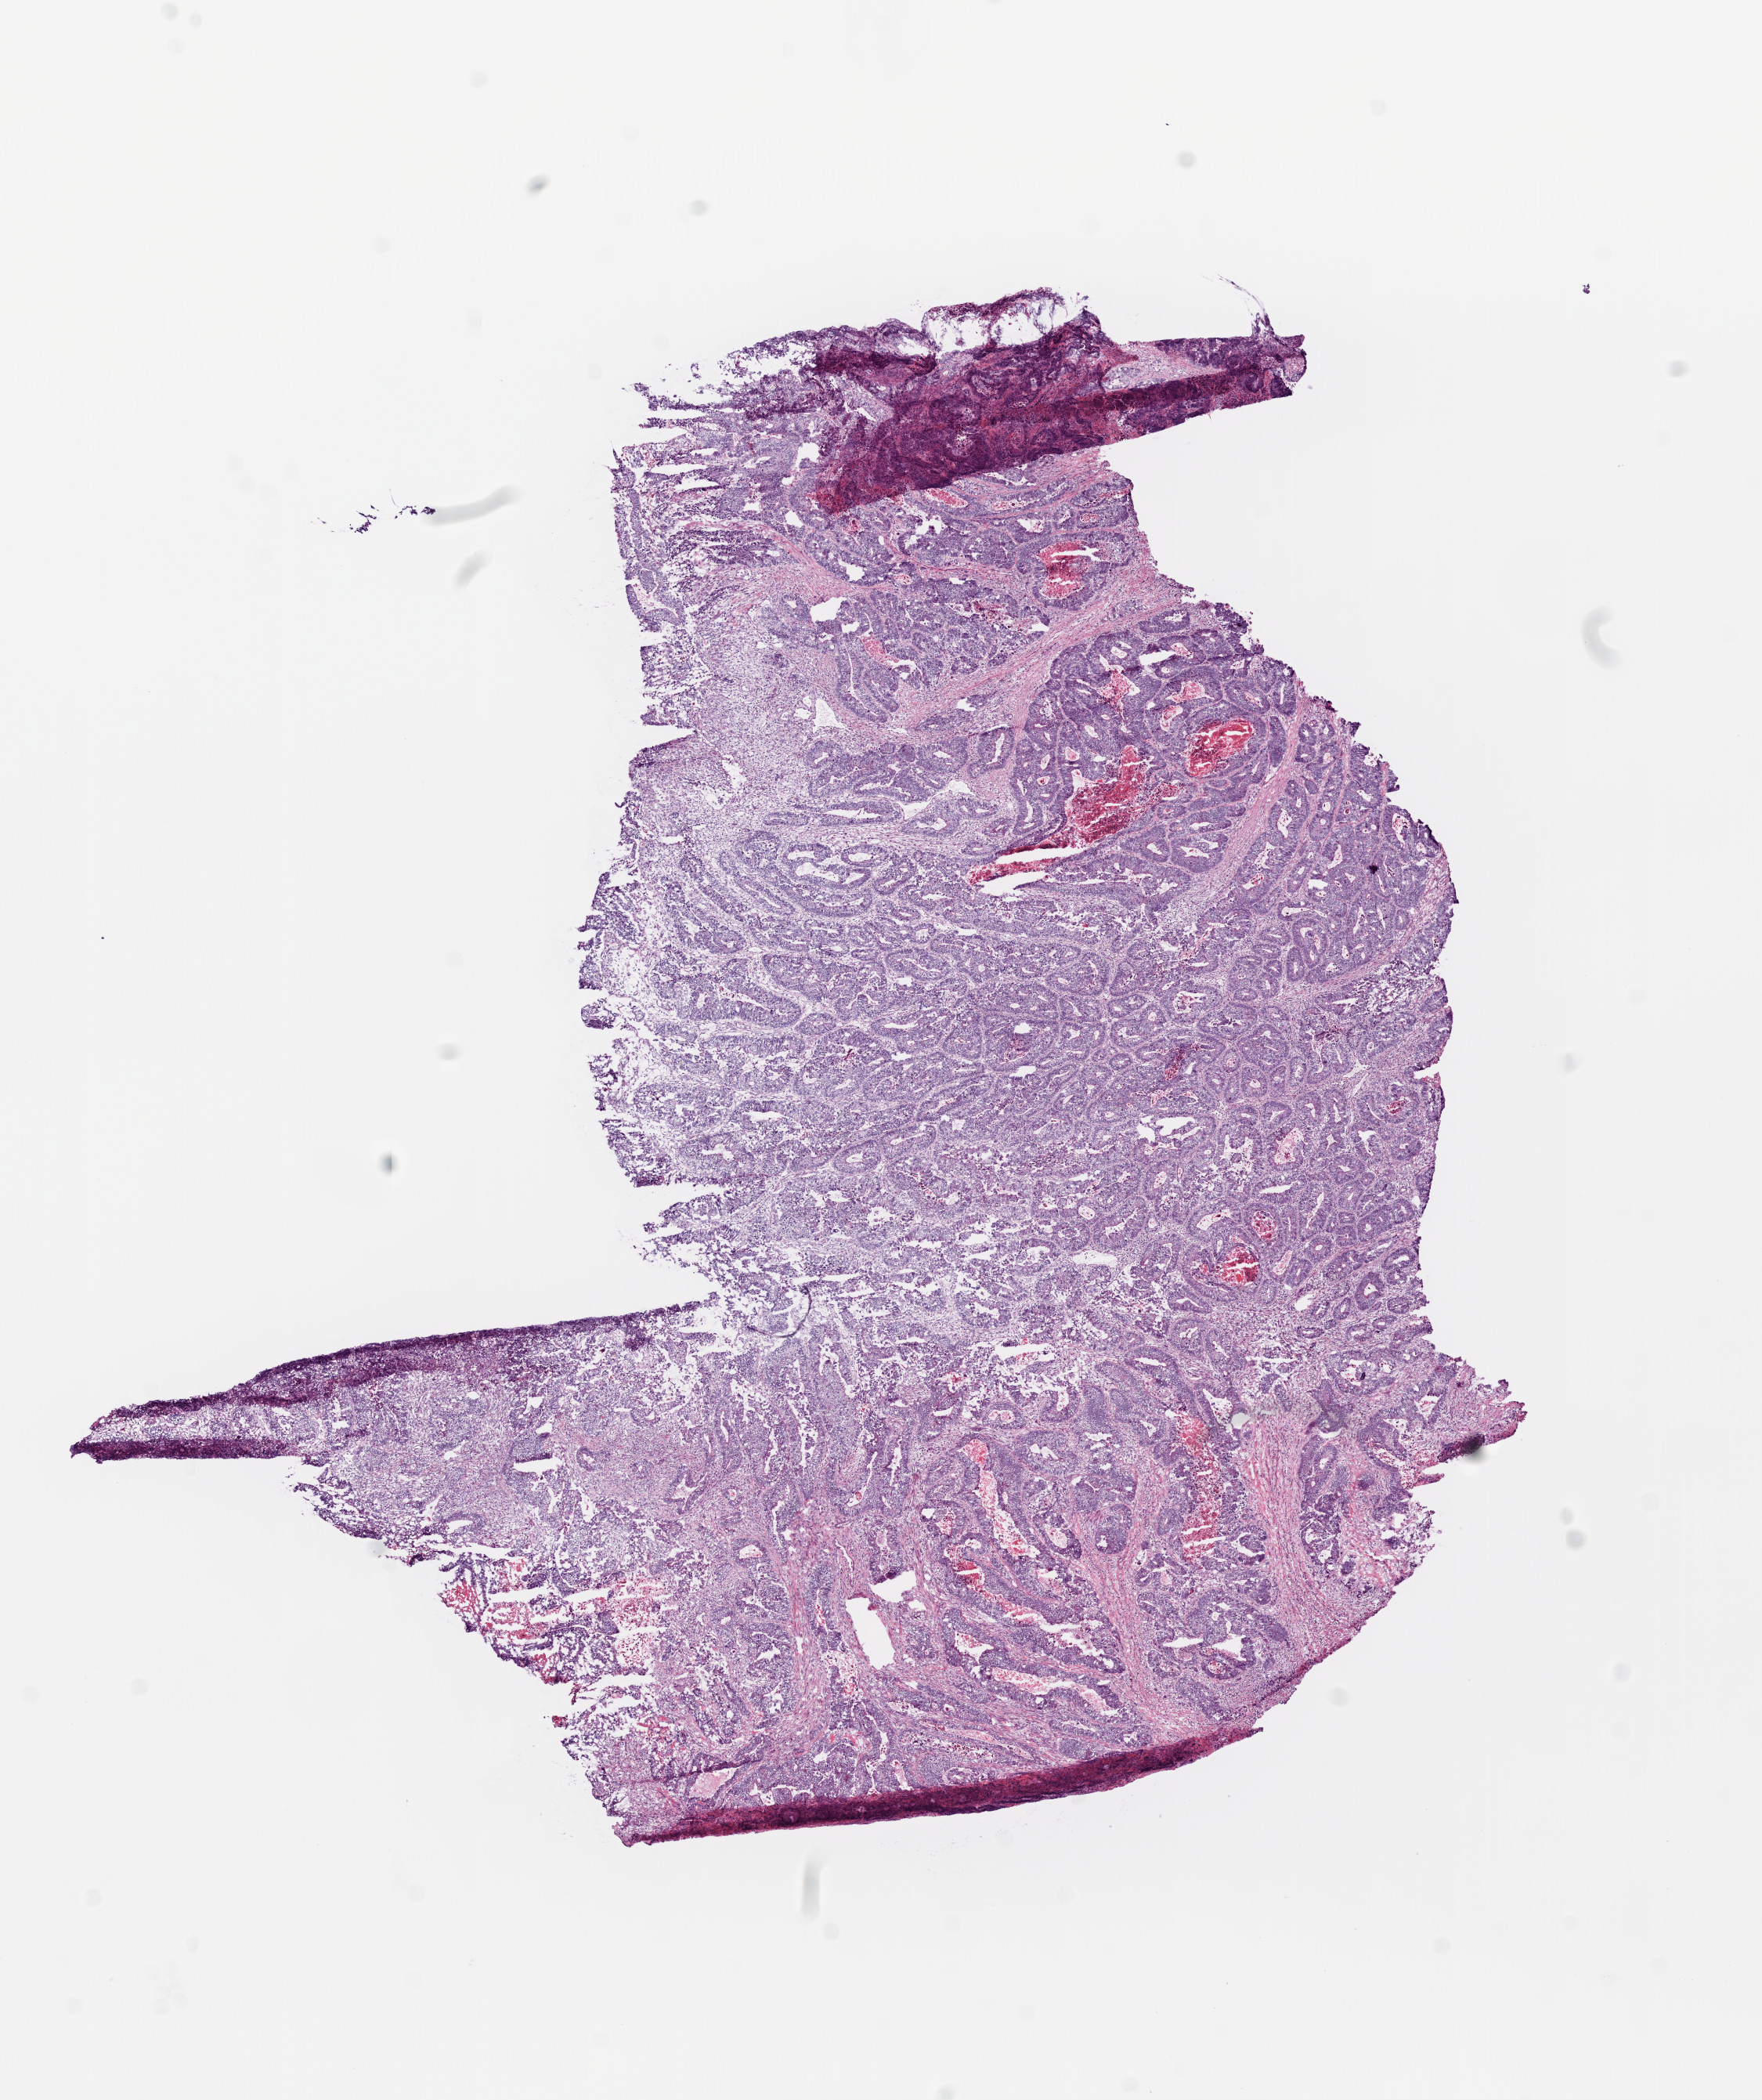
Digitized H&E tissue section (whole slide) — shown as a low-resolution overview of the whole scanned area (about 9.0 x 10.8 mm). Frozen section. Sample: primary tumour, rectum. Male, age 68 years at initial diagnosis. Slide review estimates, as recorded: tumour cells 80%, tumour nuclei 85%, normal cells 10%, stromal cells 5%, necrosis 5%.
Lymph nodes positive (case pathology): 2 of 17 examined. AJCC pathologic stage: IIIB (6th edition). Pathologic diagnosis: Adenocarcinoma, NOS (rectosigmoid junction).